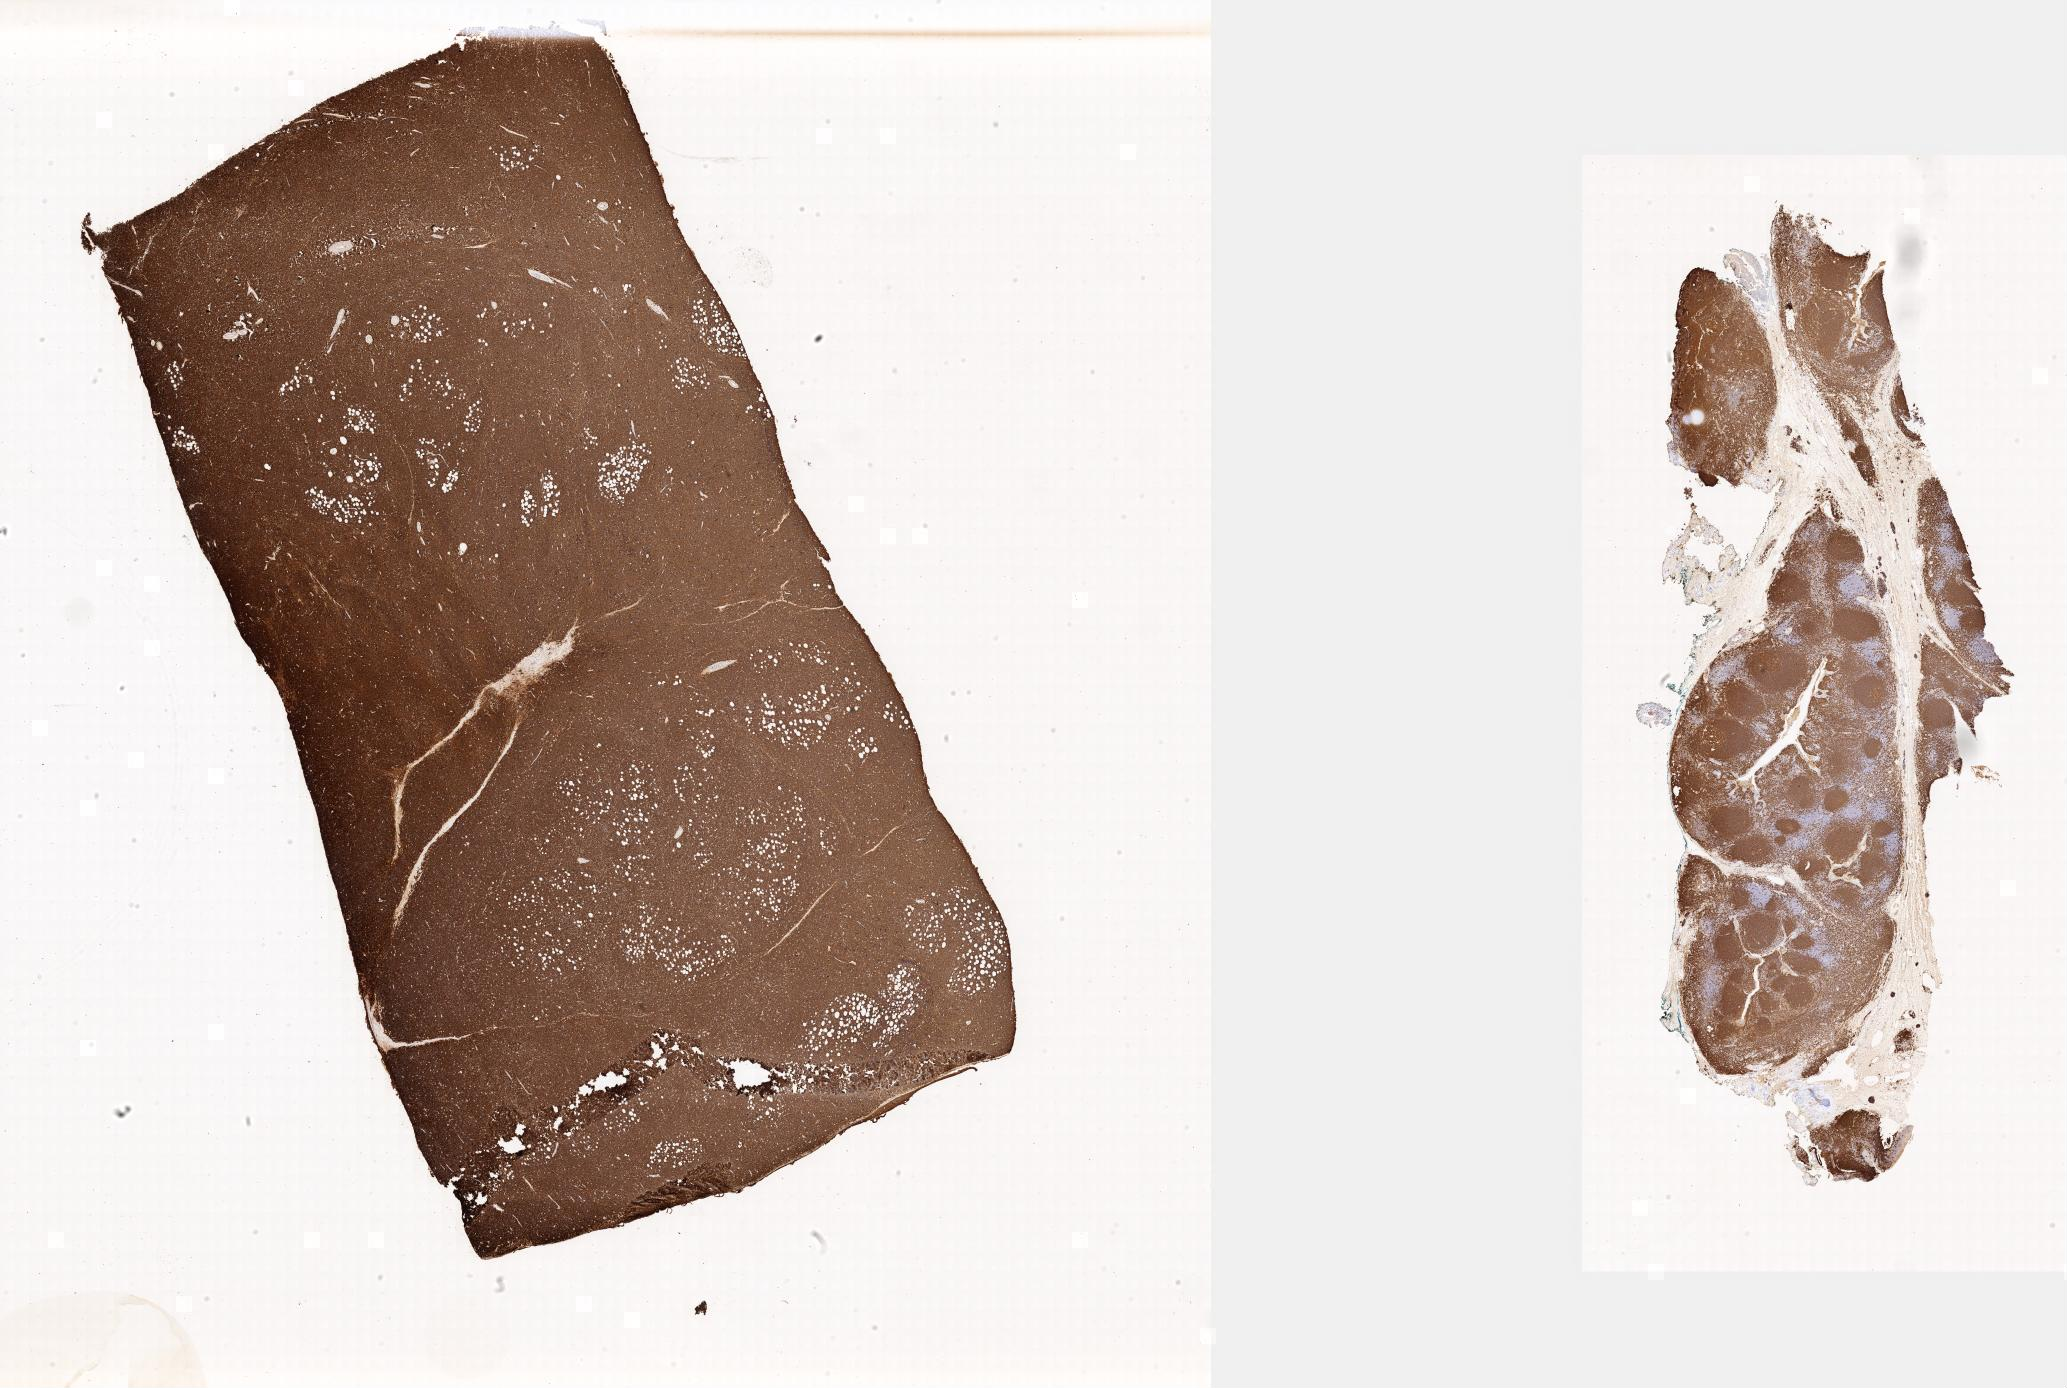
IHC for CD20, whole-slide image, shown as a low-resolution overview of the whole scanned area. Tumor tissue. Anatomic site: colon. Female patient, age 12 years.
Histologic diagnosis: Burkitt lymphoma, NOS.